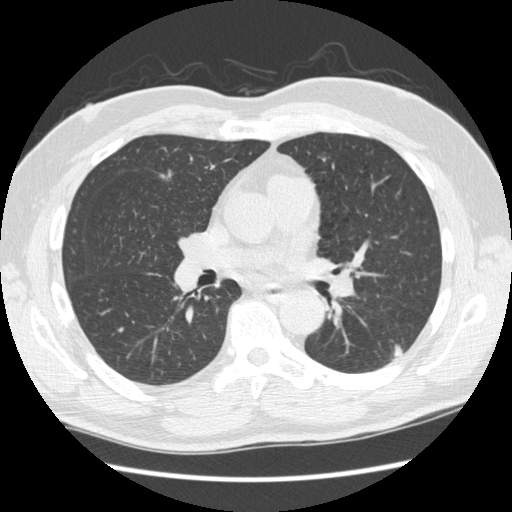
Chest CT (low-dose screening protocol), one axial image; first (baseline) screen; lung window (W 1500 / L -600 HU); 1.25 mm slice thickness; standard (soft-tissue) reconstruction kernel (STANDARD). Male, age 74 years at enrolment. Former smoker at enrolment.
Expert-annotated lung lesion, bounding box <372,324,414,367> (left, top, right, bottom; pixels). The screening reader recorded 3 non-calcified nodules or masses ≥4 mm on this exam; which of them this box marks is not recorded. Official screen result: positive, change unspecified: nodule(s) >= 4 mm or enlarging nodule(s), mass(es), or other non-specific abnormalities suspicious for lung cancer. Lung cancer was diagnosed 384 days after this screen (after the second annual screen): squamous cell carcinoma, NOS, left lower lobe, well differentiated (G1), stage IA (AJCC 6th edition), 28 mm at pathology.